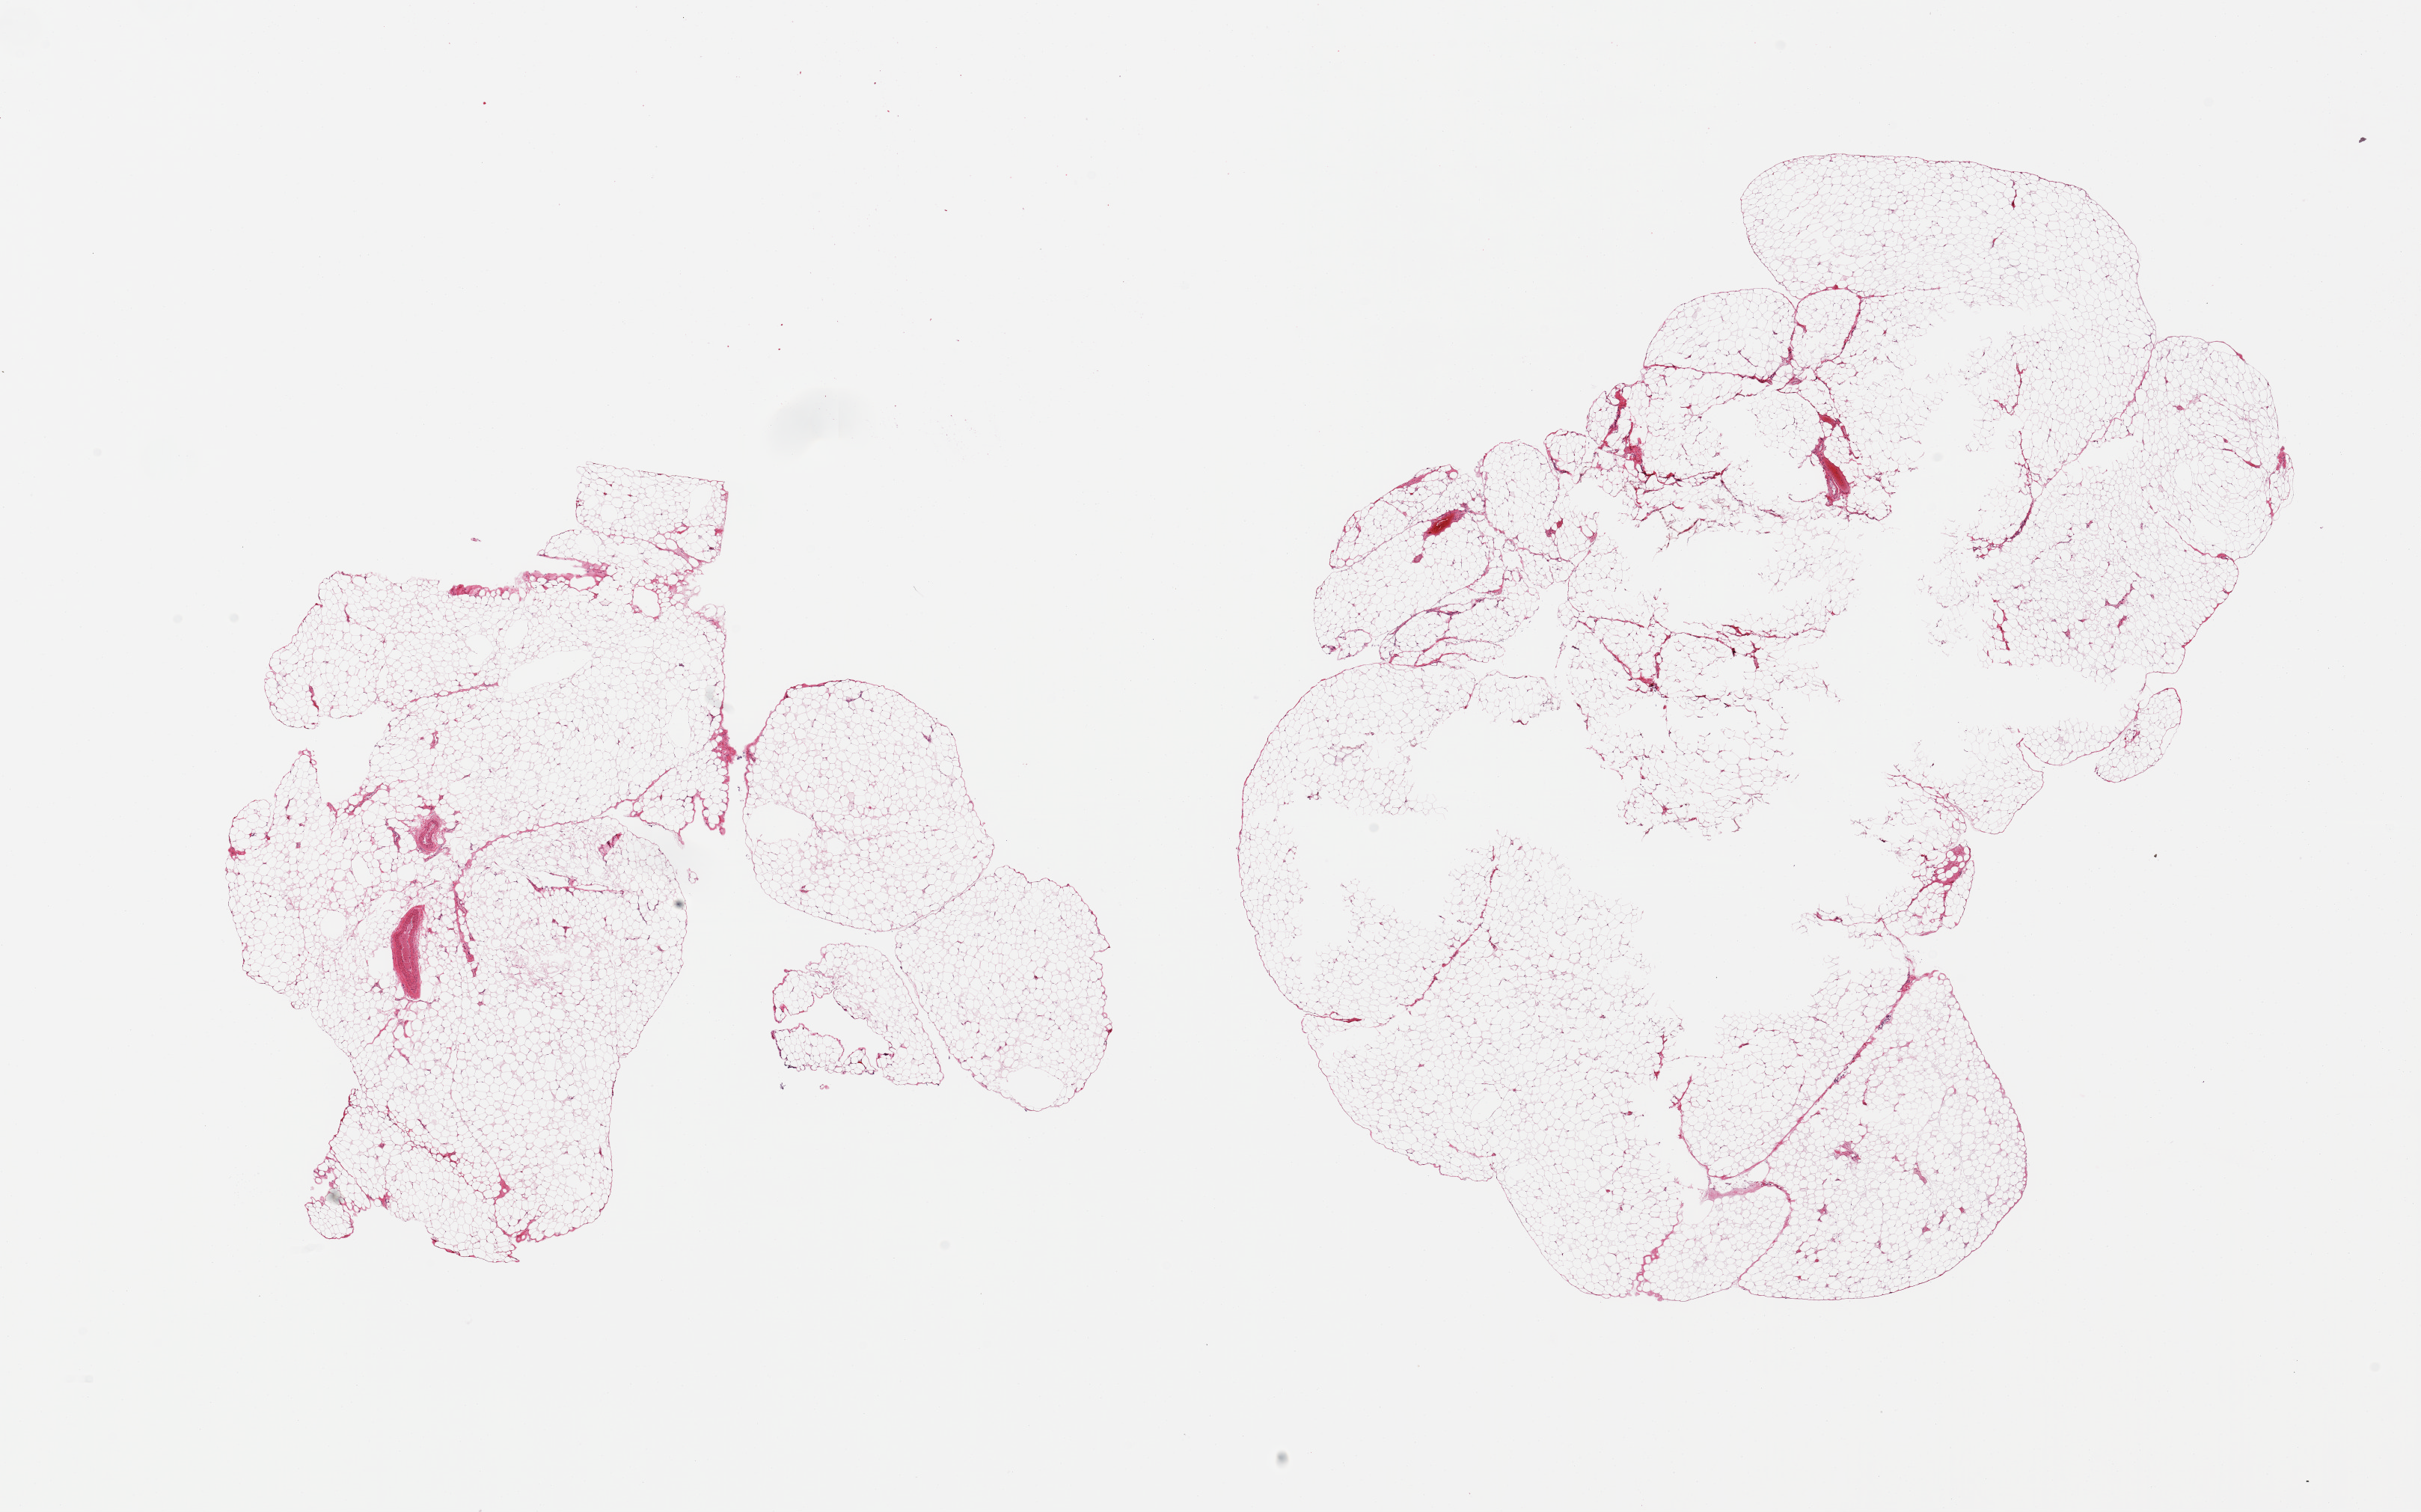
Whole-slide image, H&E stain, shown as a low-resolution overview of the whole scanned area (about 25.6 x 16.0 mm, from a 20x scan); PAXgene-fixed, paraffin-embedded tissue; section of omentum (target tissue); donor tissue sample.
Review note (as recorded): 2 pieces; lobulated mature fat, some central defects (?poor fixation).